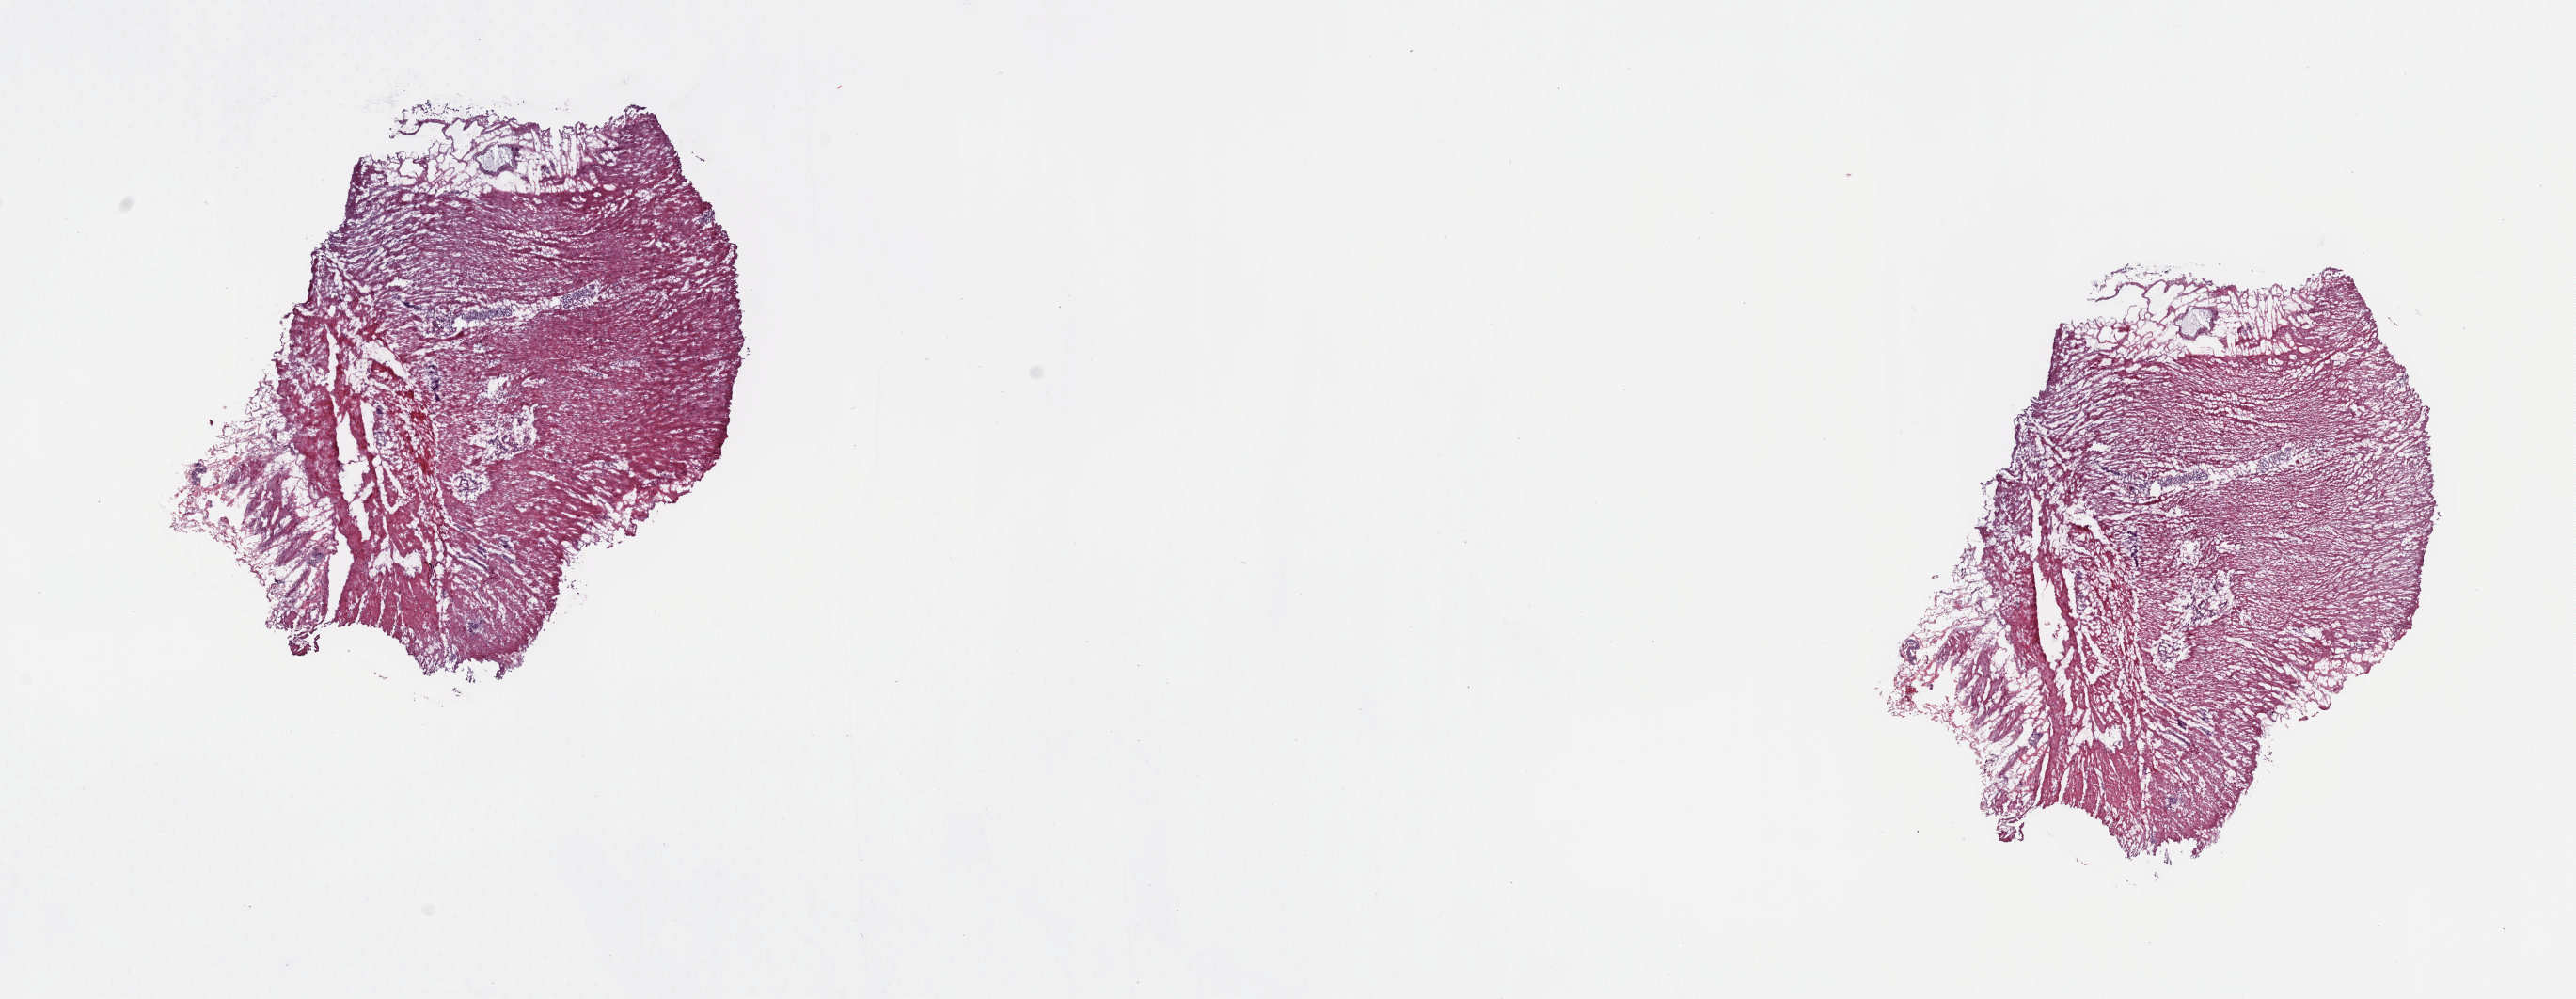
H&E whole-slide image — whole scanned area (about 21.6 x 8.4 mm, acquisition: 20x scan) shown as a low-resolution overview; frozen section; solid tissue normal (non-tumour tissue) sample from the stomach. Male patient; age at initial diagnosis 74 years. Pathologist review of this section (percent, as recorded): tumour cells 0%, tumour nuclei 0%, normal cells 0%, stromal cells 100%, necrosis 0%. Infiltration values recorded for this section: lymphocyte infiltration 2%, monocyte infiltration 1%, neutrophil infiltration 1%.
• this section: solid tissue normal (non-tumour) sample from the same patient
• patient diagnosis: Carcinoma, diffuse type (gastric antrum)